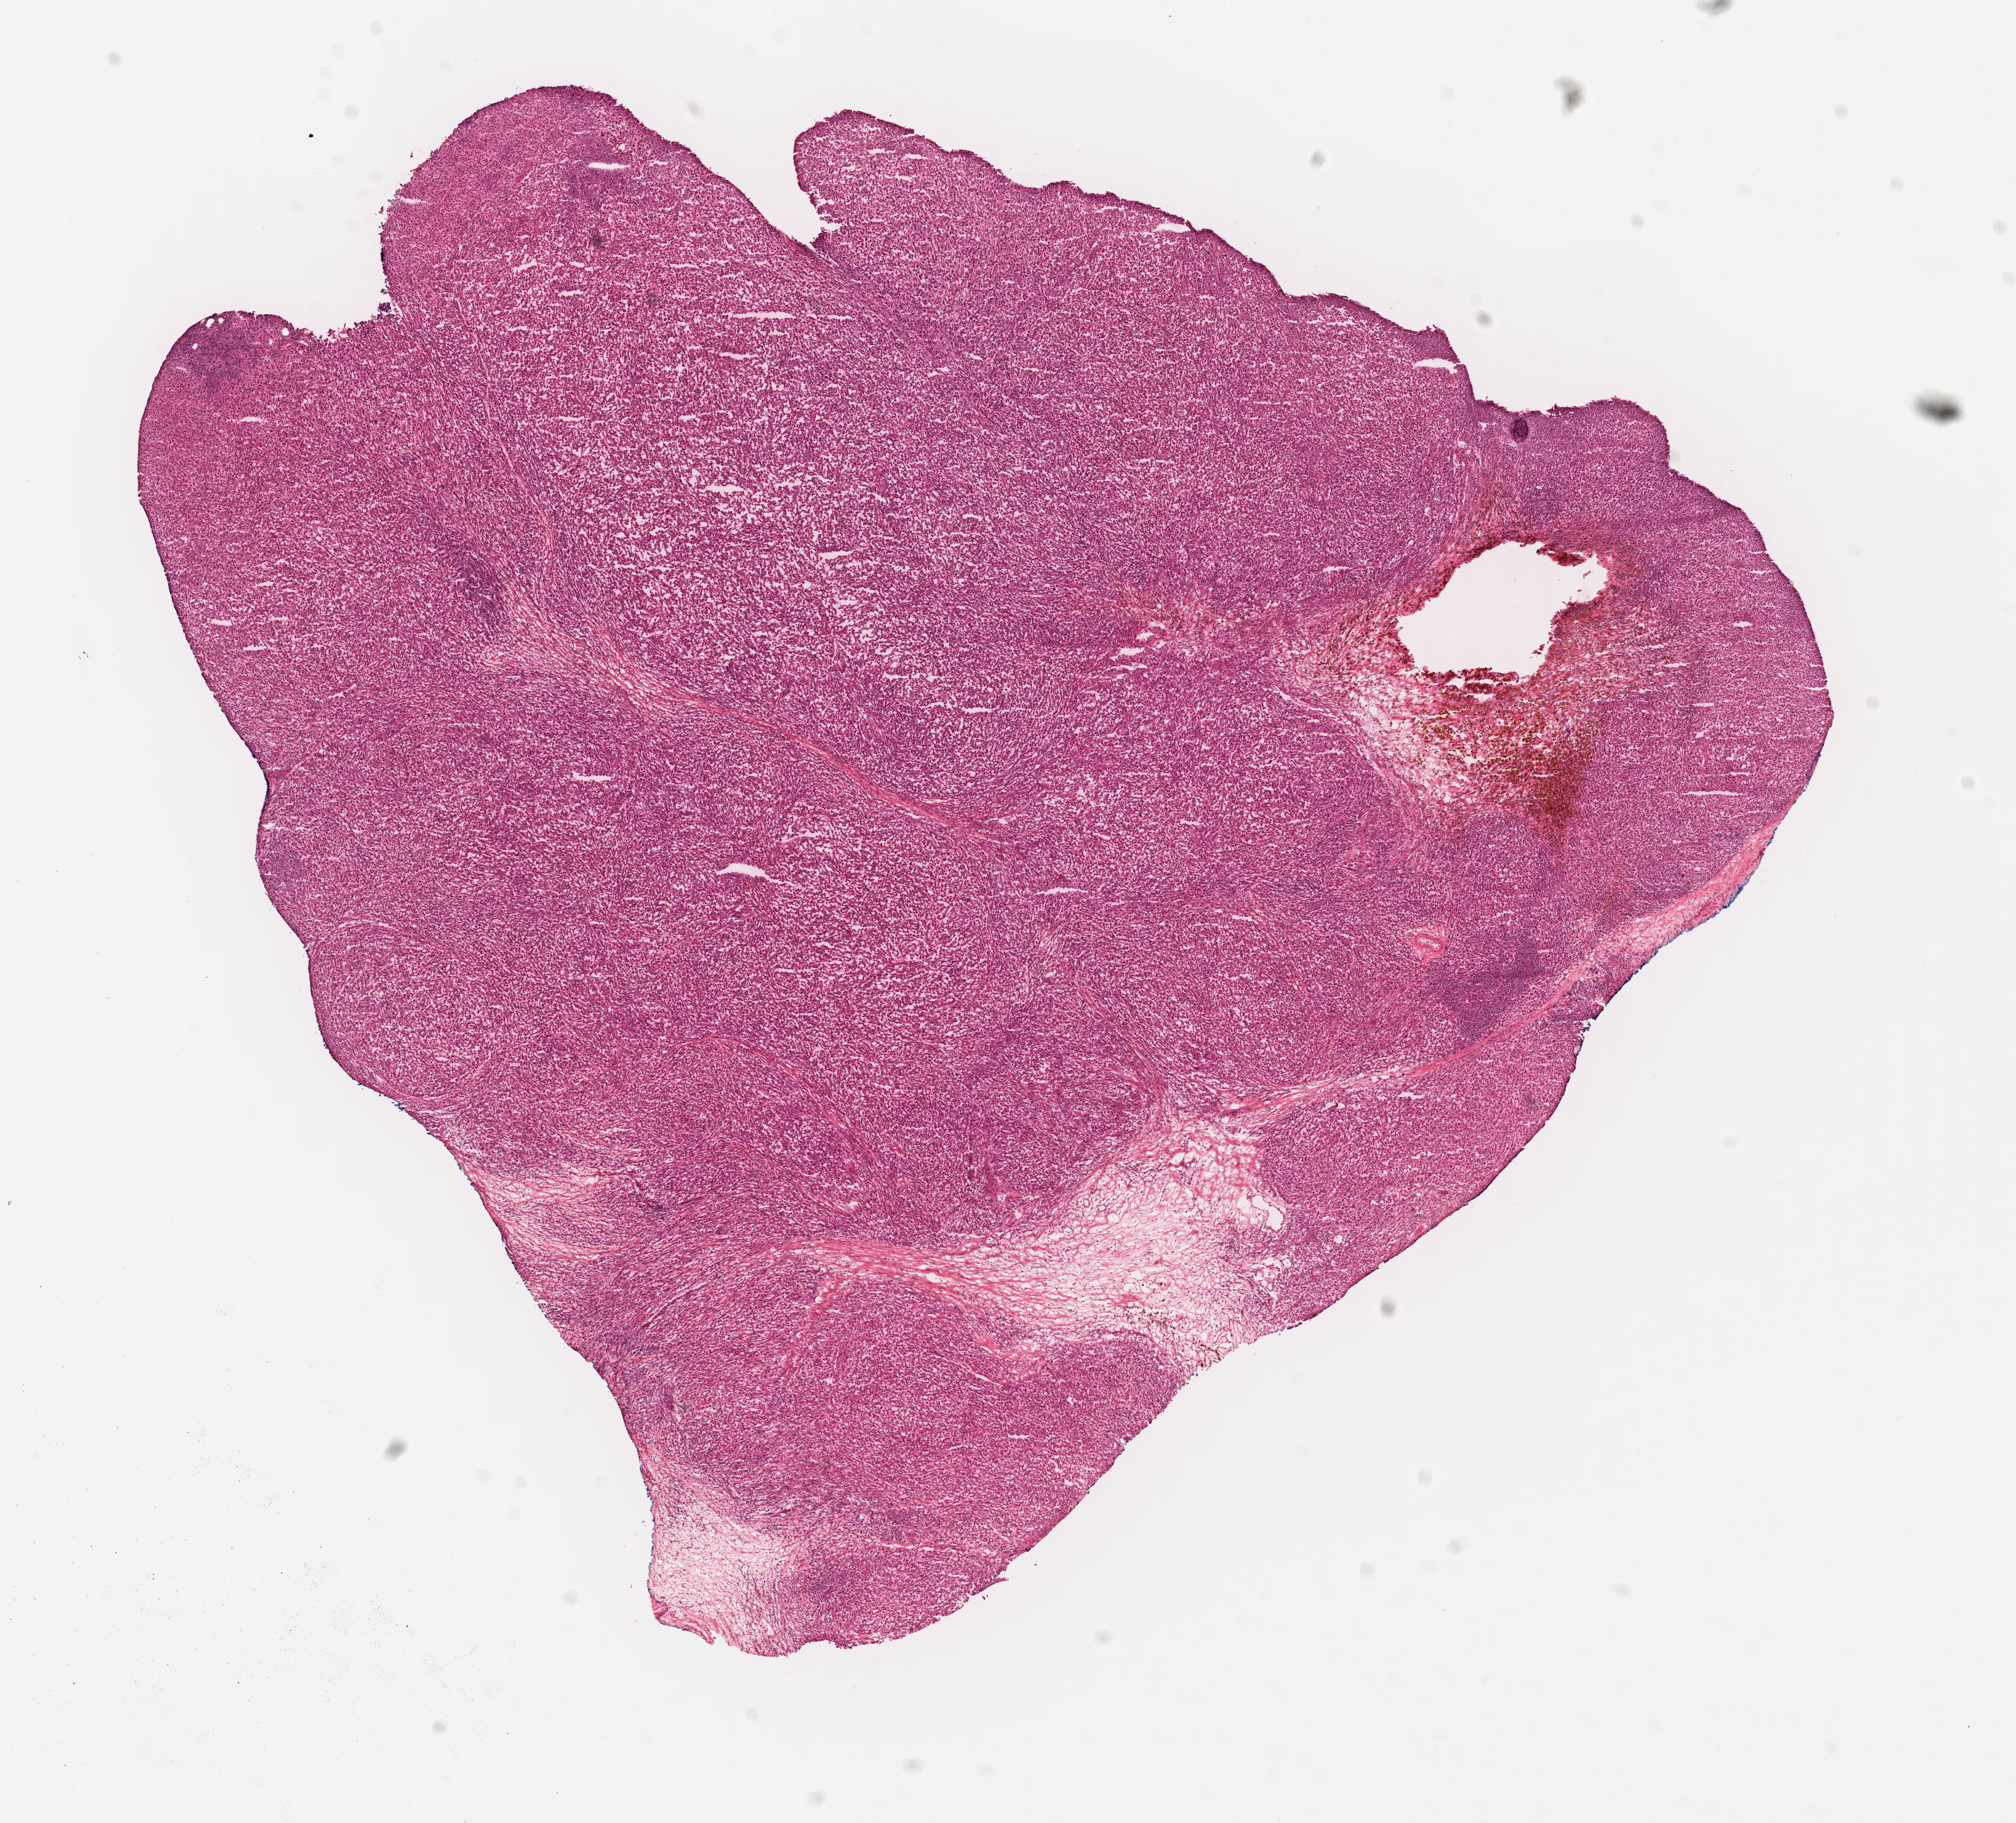
Whole-slide histology image, Hematoxylin and eosin (H&E) stained, shown as a low-resolution overview of the whole scanned area (about 12.6 x 11.4 mm, from a 40x scan); FFPE section; metastatic tumour sample. Male, age 44 years at initial diagnosis.
This section: metastatic tumour tissue. Patient diagnosis: Malignant melanoma, NOS.